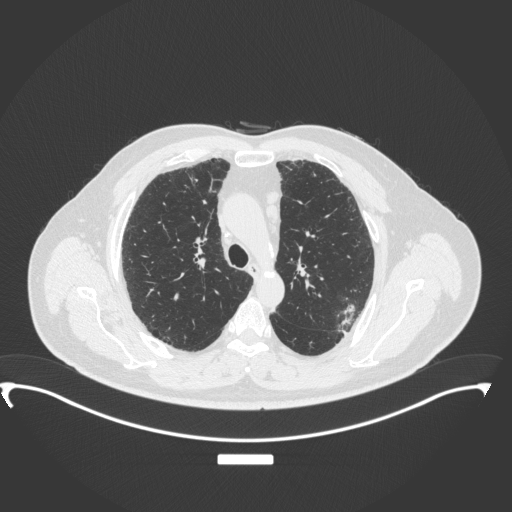
Chest CT, one axial slice; position 254 of 350 along the scan axis; reconstruction kernel B31f; 120 kVp; lung window (W 1500 / L -600 HU); 1 mm slice thickness; 512 × 512 image matrix, field of view 459 × 459 mm. Male patient, age 64 years. From the clinical record (not read from this slice): clinical TNM (as recorded): T1c N1 M1.
Structures marked on this image (bounding box drawn by a radiologist):
- lung tumour (recorded histology: adenocarcinoma): bounding box [x1, y1, x2, y2] px = [334, 303, 359, 335]